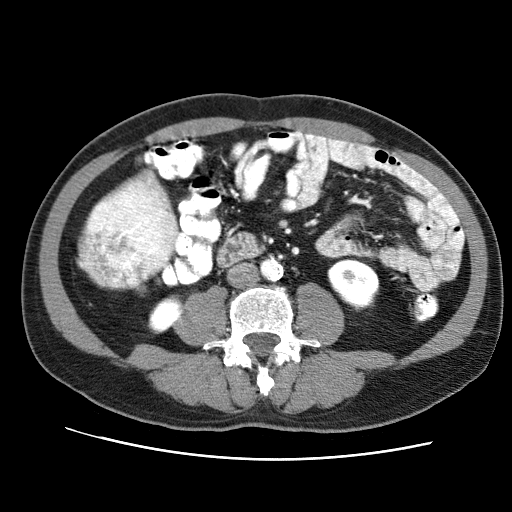
Contrast-enhanced abdominal CT (liver protocol), one axial slice; slice 10 of 71 in the series (ordered by position); soft-tissue window (W 400 / L 40 HU); 2.5 mm slice thickness; 512 × 512 image matrix. Case-level facts recorded for this patient, not image findings: diagnosis: hepatocellular carcinoma (patient treated with transarterial chemoembolisation; whether this scan precedes or follows treatment is not stated here); TNM stage (as recorded): Stage-II; Child-Pugh class: A; tumour differentiation: well differentiated; tumour nodularity: multinodular.
Structures marked on this image (semi-automatically segmented with operator editing):
- liver parenchyma outside the tumour (the mass and vessels are separate outlines, so this box may not span the whole liver): bounding box [x1, y1, x2, y2] px = [77, 177, 180, 289]
- mass: [76, 169, 180, 289]